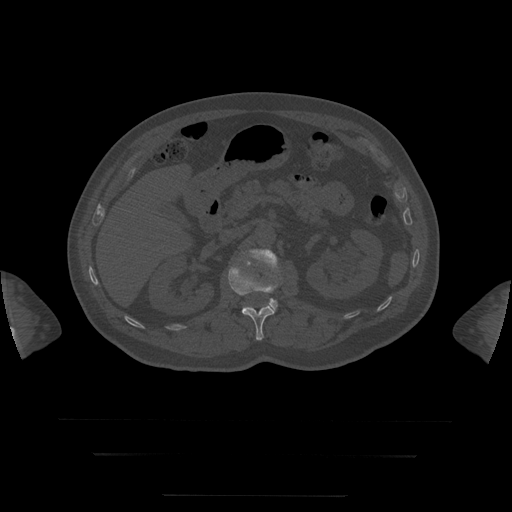
CT including the spine, one axial slice; slice 40 of 397 in the series (ordered by position); reconstruction kernel STANDARD; 120 kVp; bone window (W 1800 / L 400 HU); 1.25 mm slice thickness; 512 × 512 image matrix, field of view 510 × 510 mm. Patient age 73 years. From the clinical record (not read from this slice): primary cancer: prostate.
Outlined on this slice (semi-automatically segmented with operator editing):
- L1 vertebra: bounding box [x1, y1, x2, y2] px = [228, 259, 278, 341]